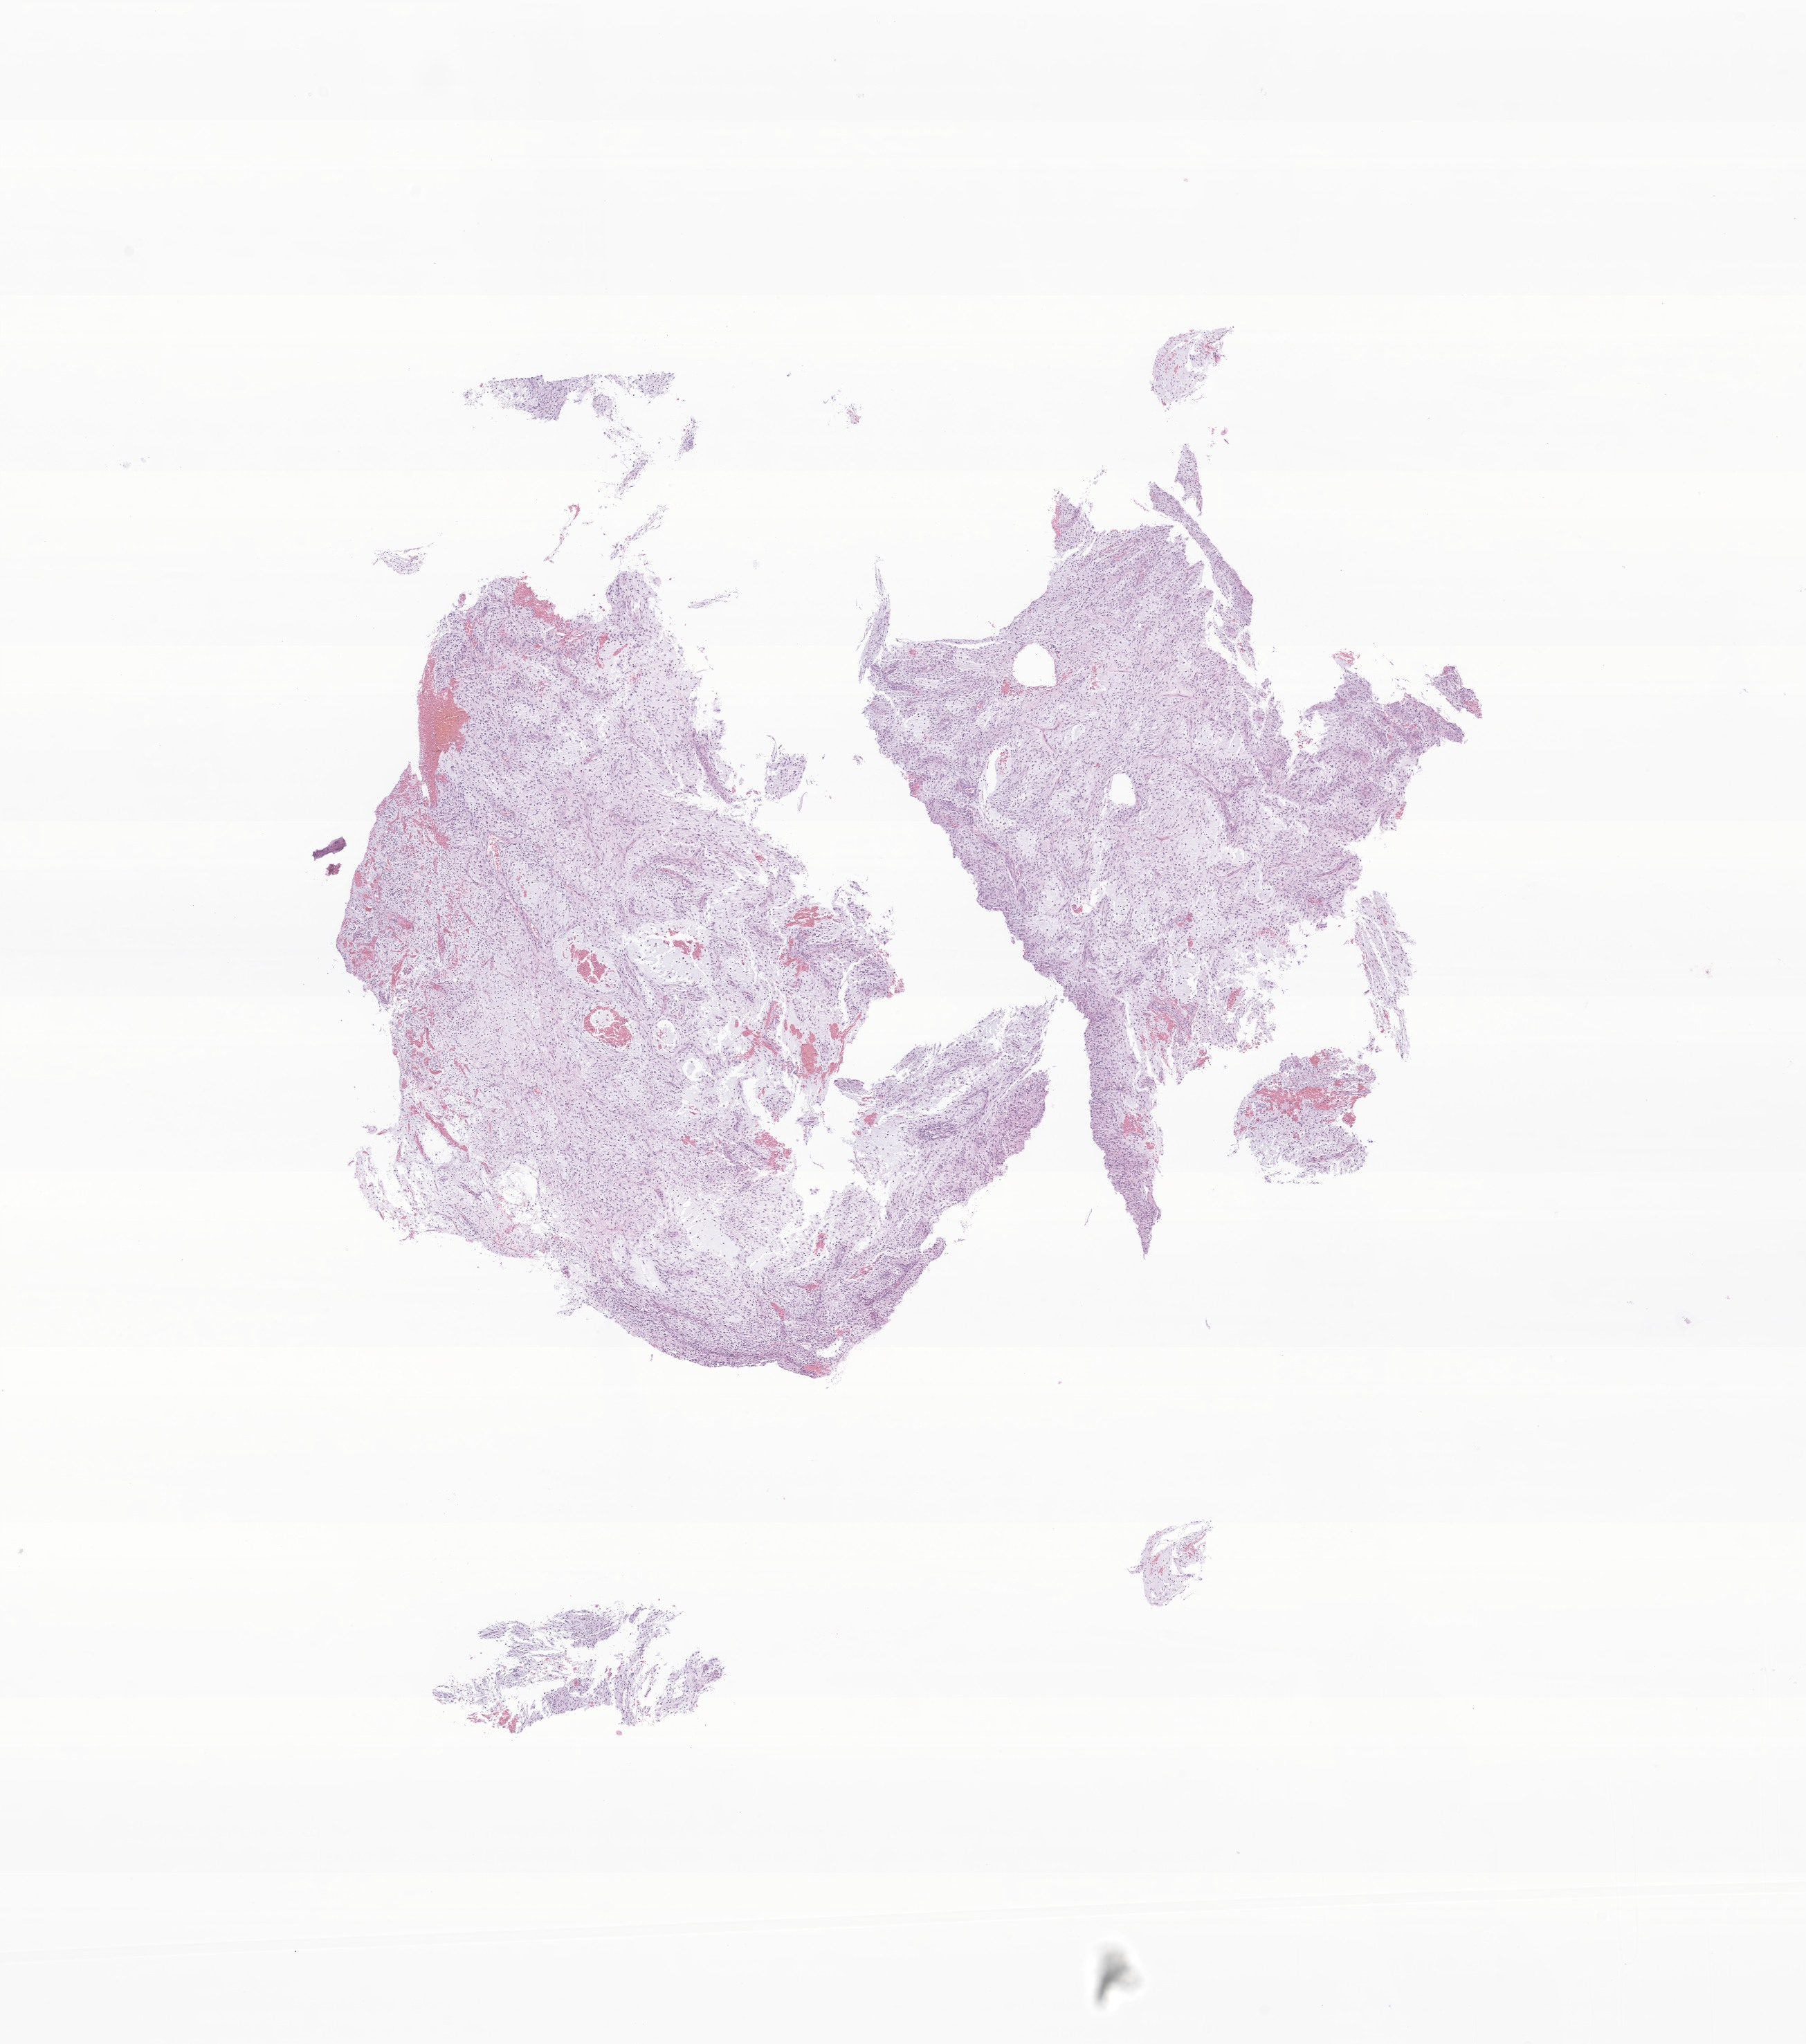
Whole-slide image, H&E stain of tumor tissue from the brain, a low-resolution overview of the entire scanned area, about 11.0 x 12.5 mm. Formalin-fixed, paraffin-embedded (FFPE) tissue. Patient female; age 88 months.
Diagnosis (ICD-O-3 morphology term): Pilocytic astrocytoma.